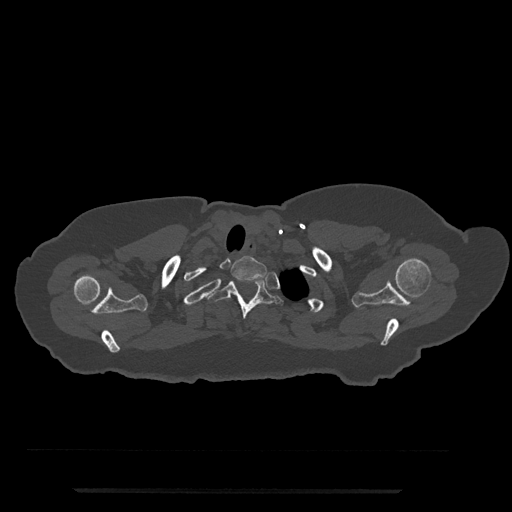
CT including the spine, one axial slice; position 685 of 797 along the scan axis; reconstruction kernel Br40s/3; bone window (W 1800 / L 400 HU); 512 × 512 image matrix. Patient: female, 51 years. Case-level facts recorded for this patient, not image findings: primary cancer: neuro; vertebrae with lytic lesions (as recorded): T8.
Structures marked on this image (semi-automatically segmented with operator editing):
- T1 vertebra: bounding box <231,256,267,281> (left, top, right, bottom; pixels)
- T2 vertebra: <206,274,284,319>